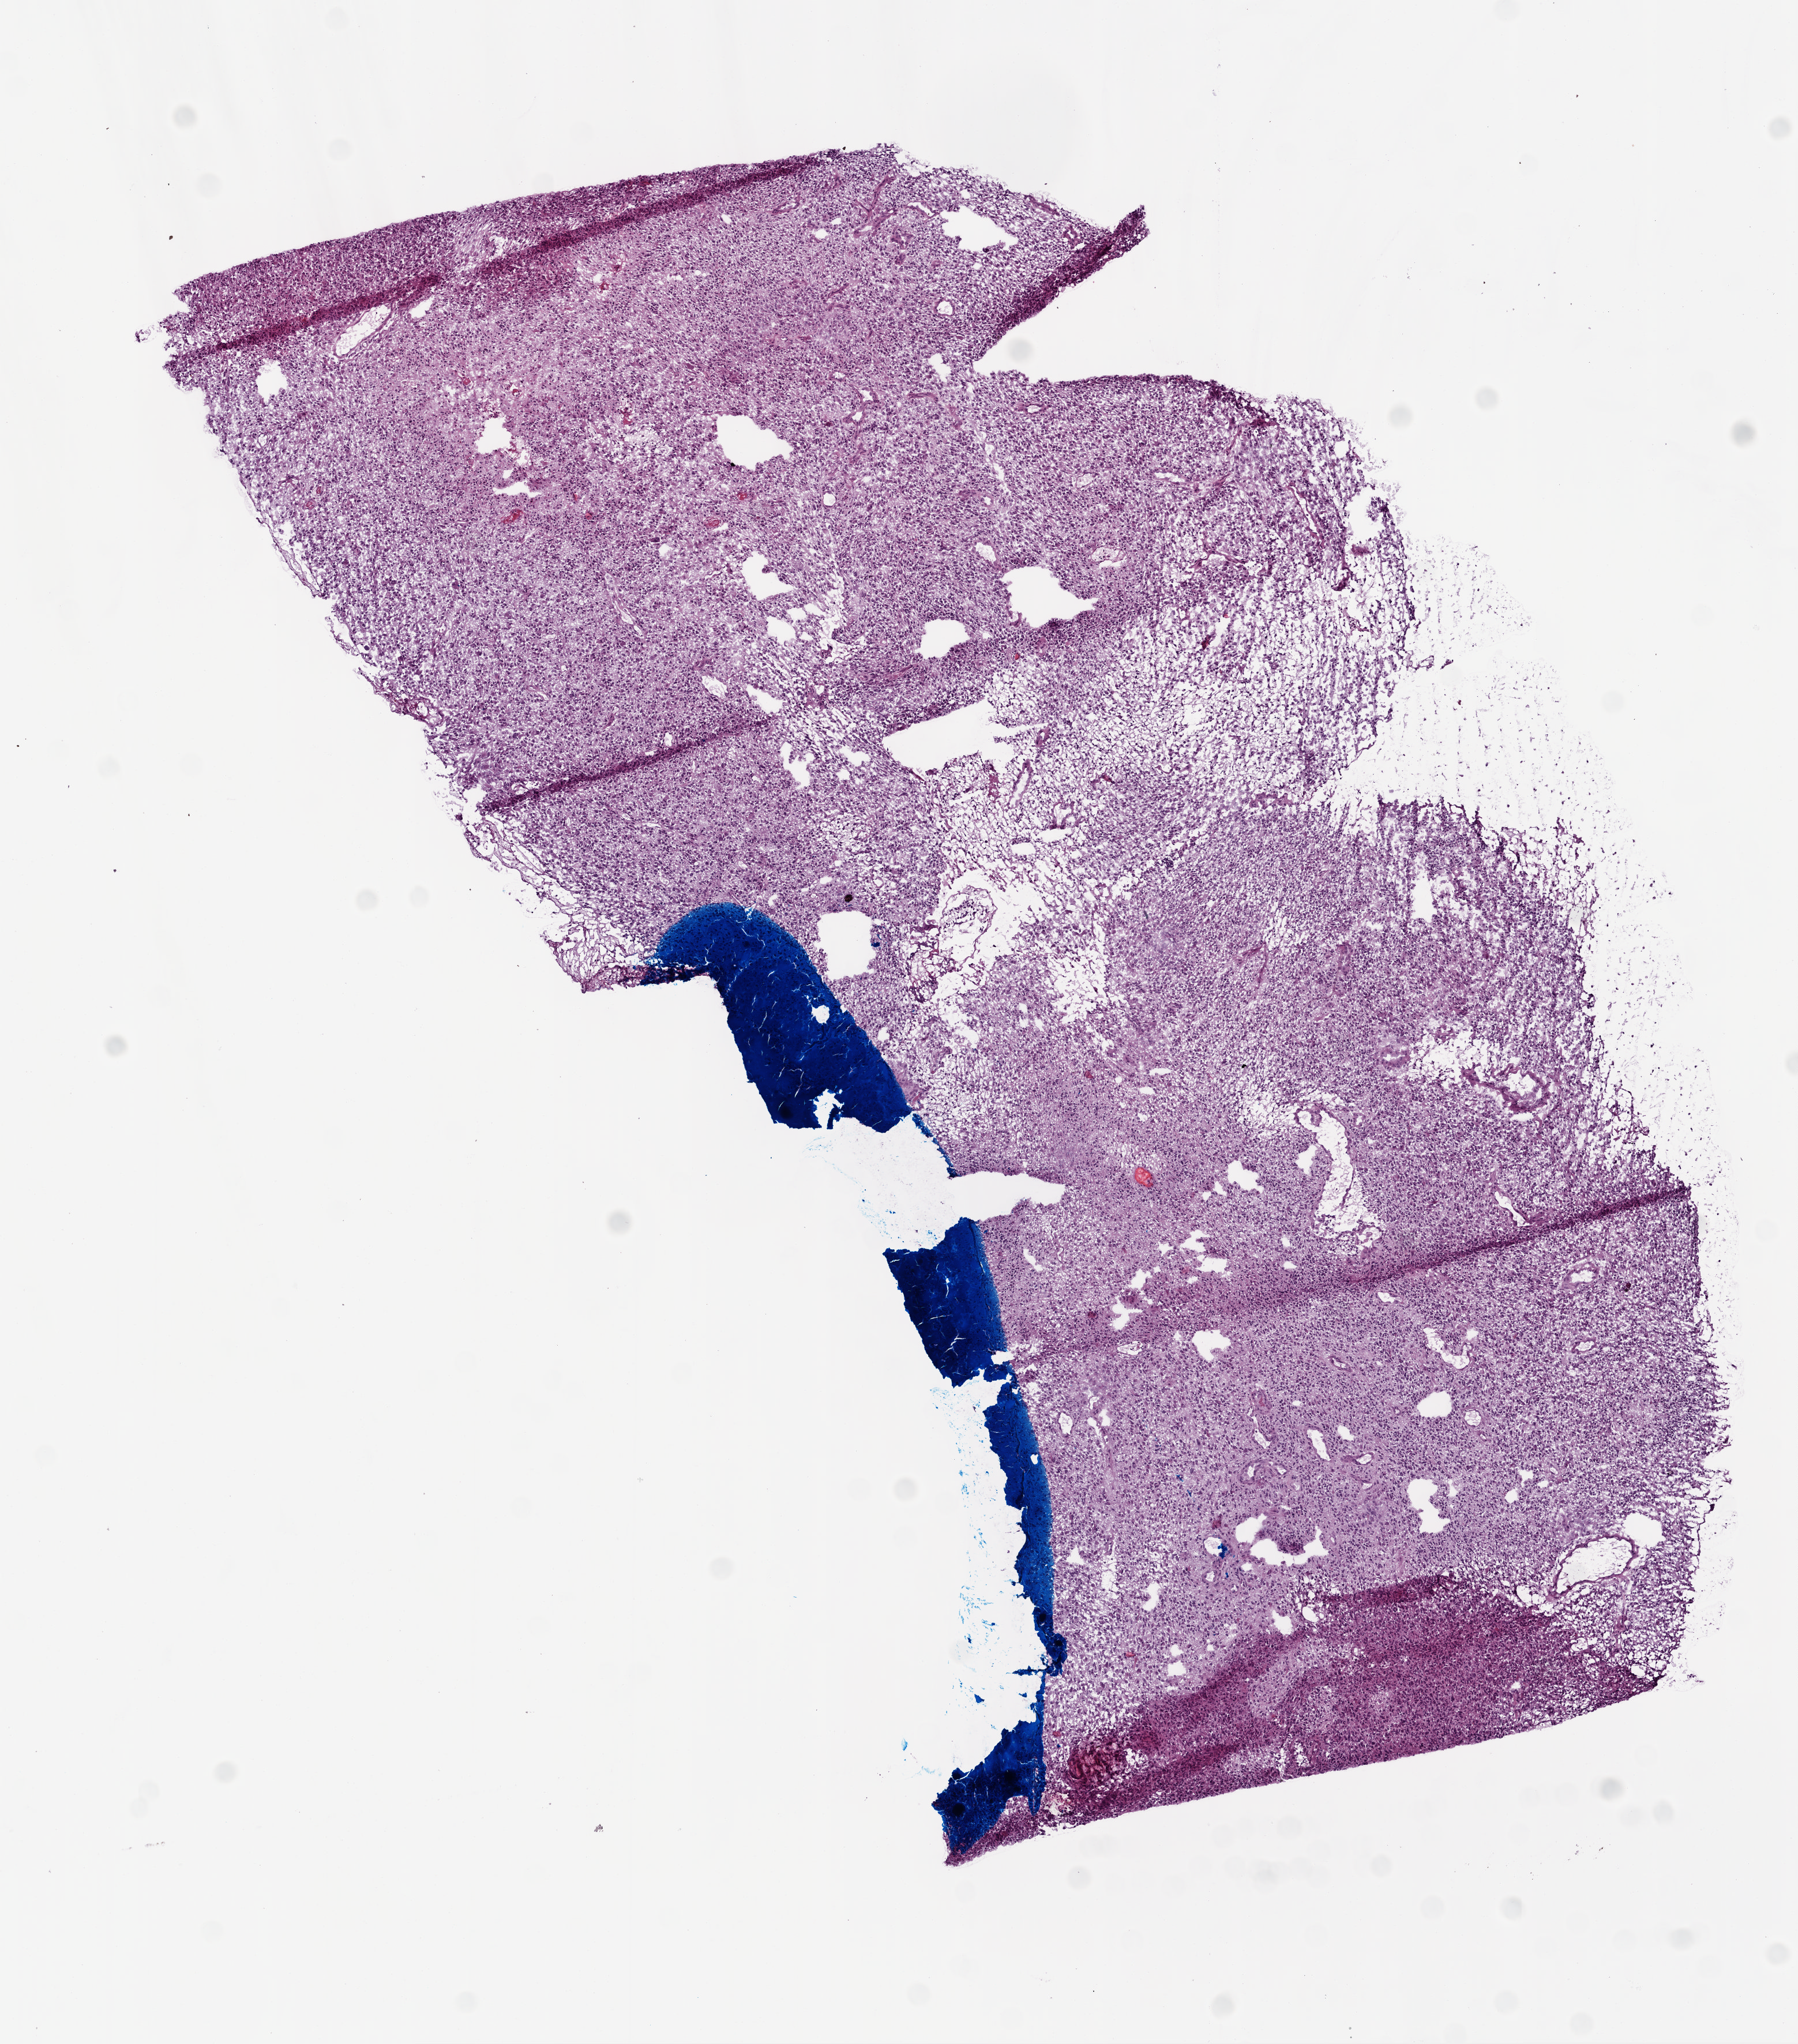
Hematoxylin and eosin (H&E) stained whole-slide image, low-resolution overview of the scanned area, about 6.3 x 7.1 mm (from a 20x scan), frozen section, primary tumour sample from the brain. Male patient; age at initial diagnosis 52 years. Composition of this section per pathologist review: tumour cells 75%, tumour nuclei 90%.
Pathologic diagnosis: Glioblastoma.